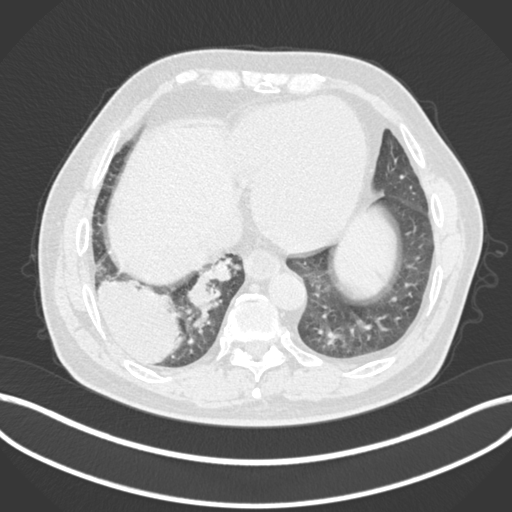
Chest CT, one axial slice. Slice 34 of 200 in the series (ordered by position). Reconstruction kernel B30f. Lung window (W 1500 / L -600 HU). 1 mm slice thickness. 512 × 512 image matrix, field of view 400 × 400 mm. Male patient, age 59 years.
Outlined on this slice (bounding box drawn by a radiologist):
- lung tumour (recorded histology: adenocarcinoma): bounding box [x1, y1, x2, y2] px = [92, 279, 189, 369]